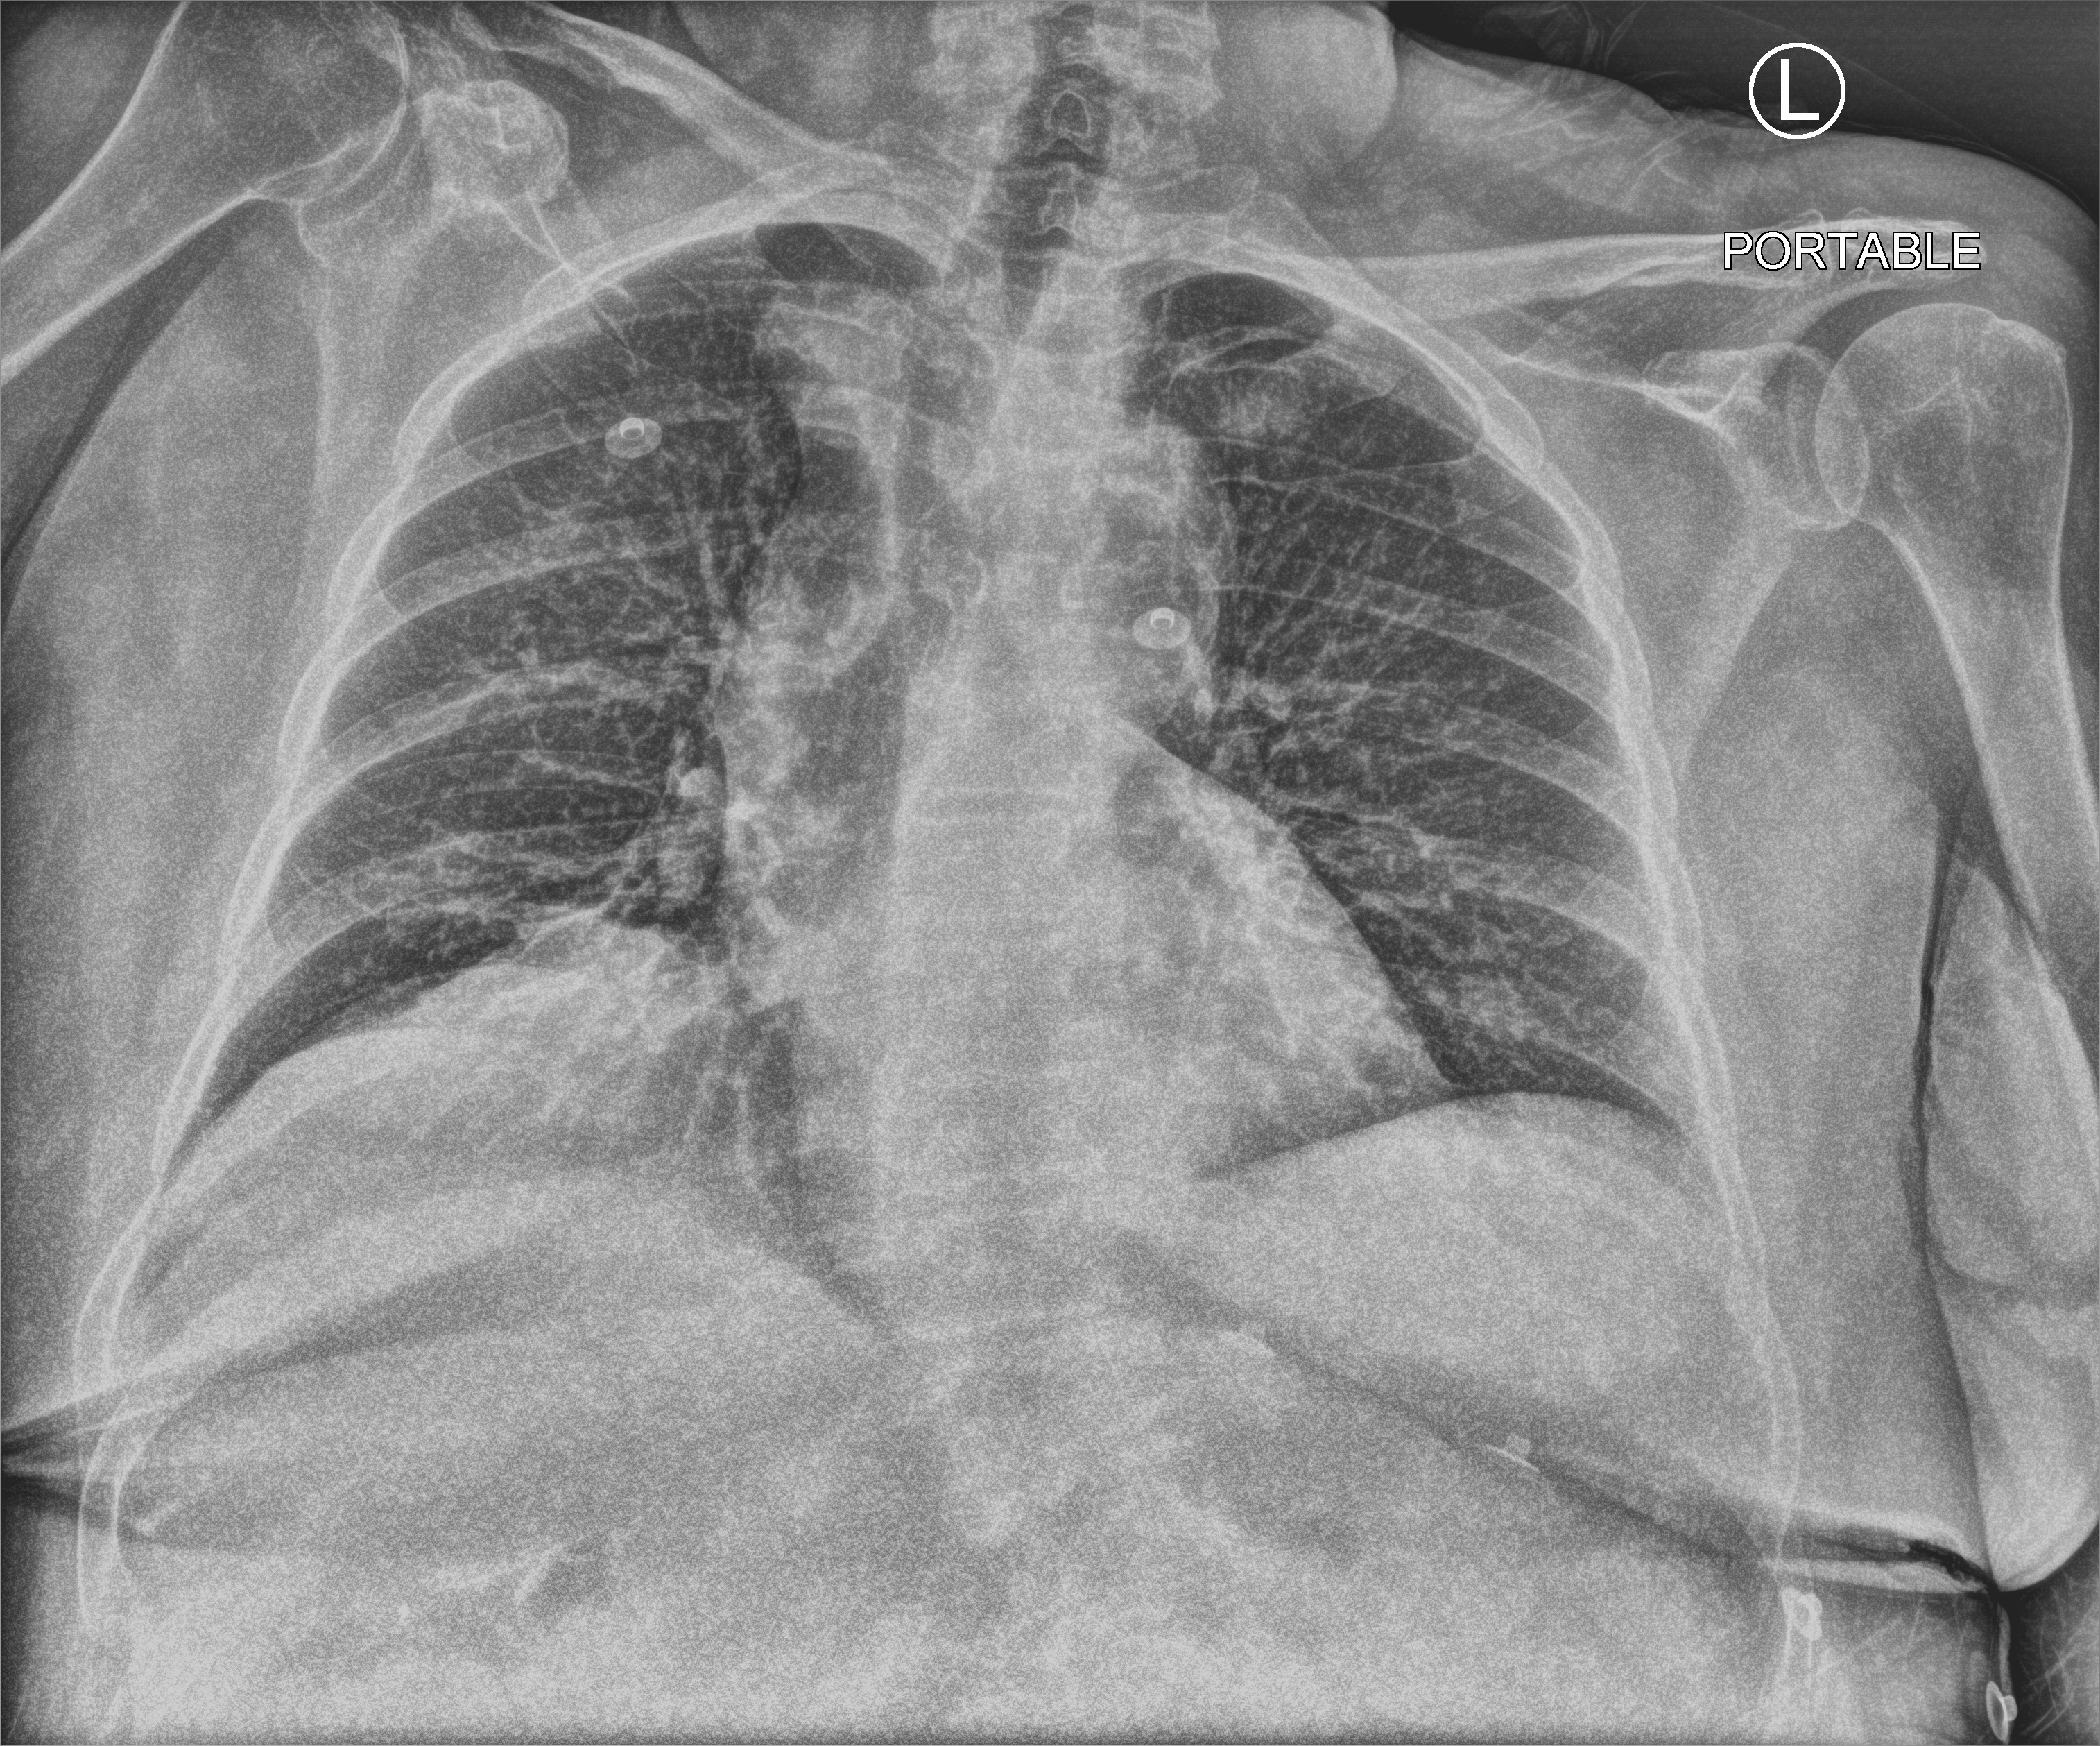
Bedside chest radiograph (computed radiography), anteroposterior (AP) projection. Patient hospitalised with COVID-19; female, aged 75–90 years.
From the hospital-stay record, not from the radiograph (when in the stay this image was taken is not recorded): hypertension (admission record): yes; admitted to intensive care during this hospital stay: no.